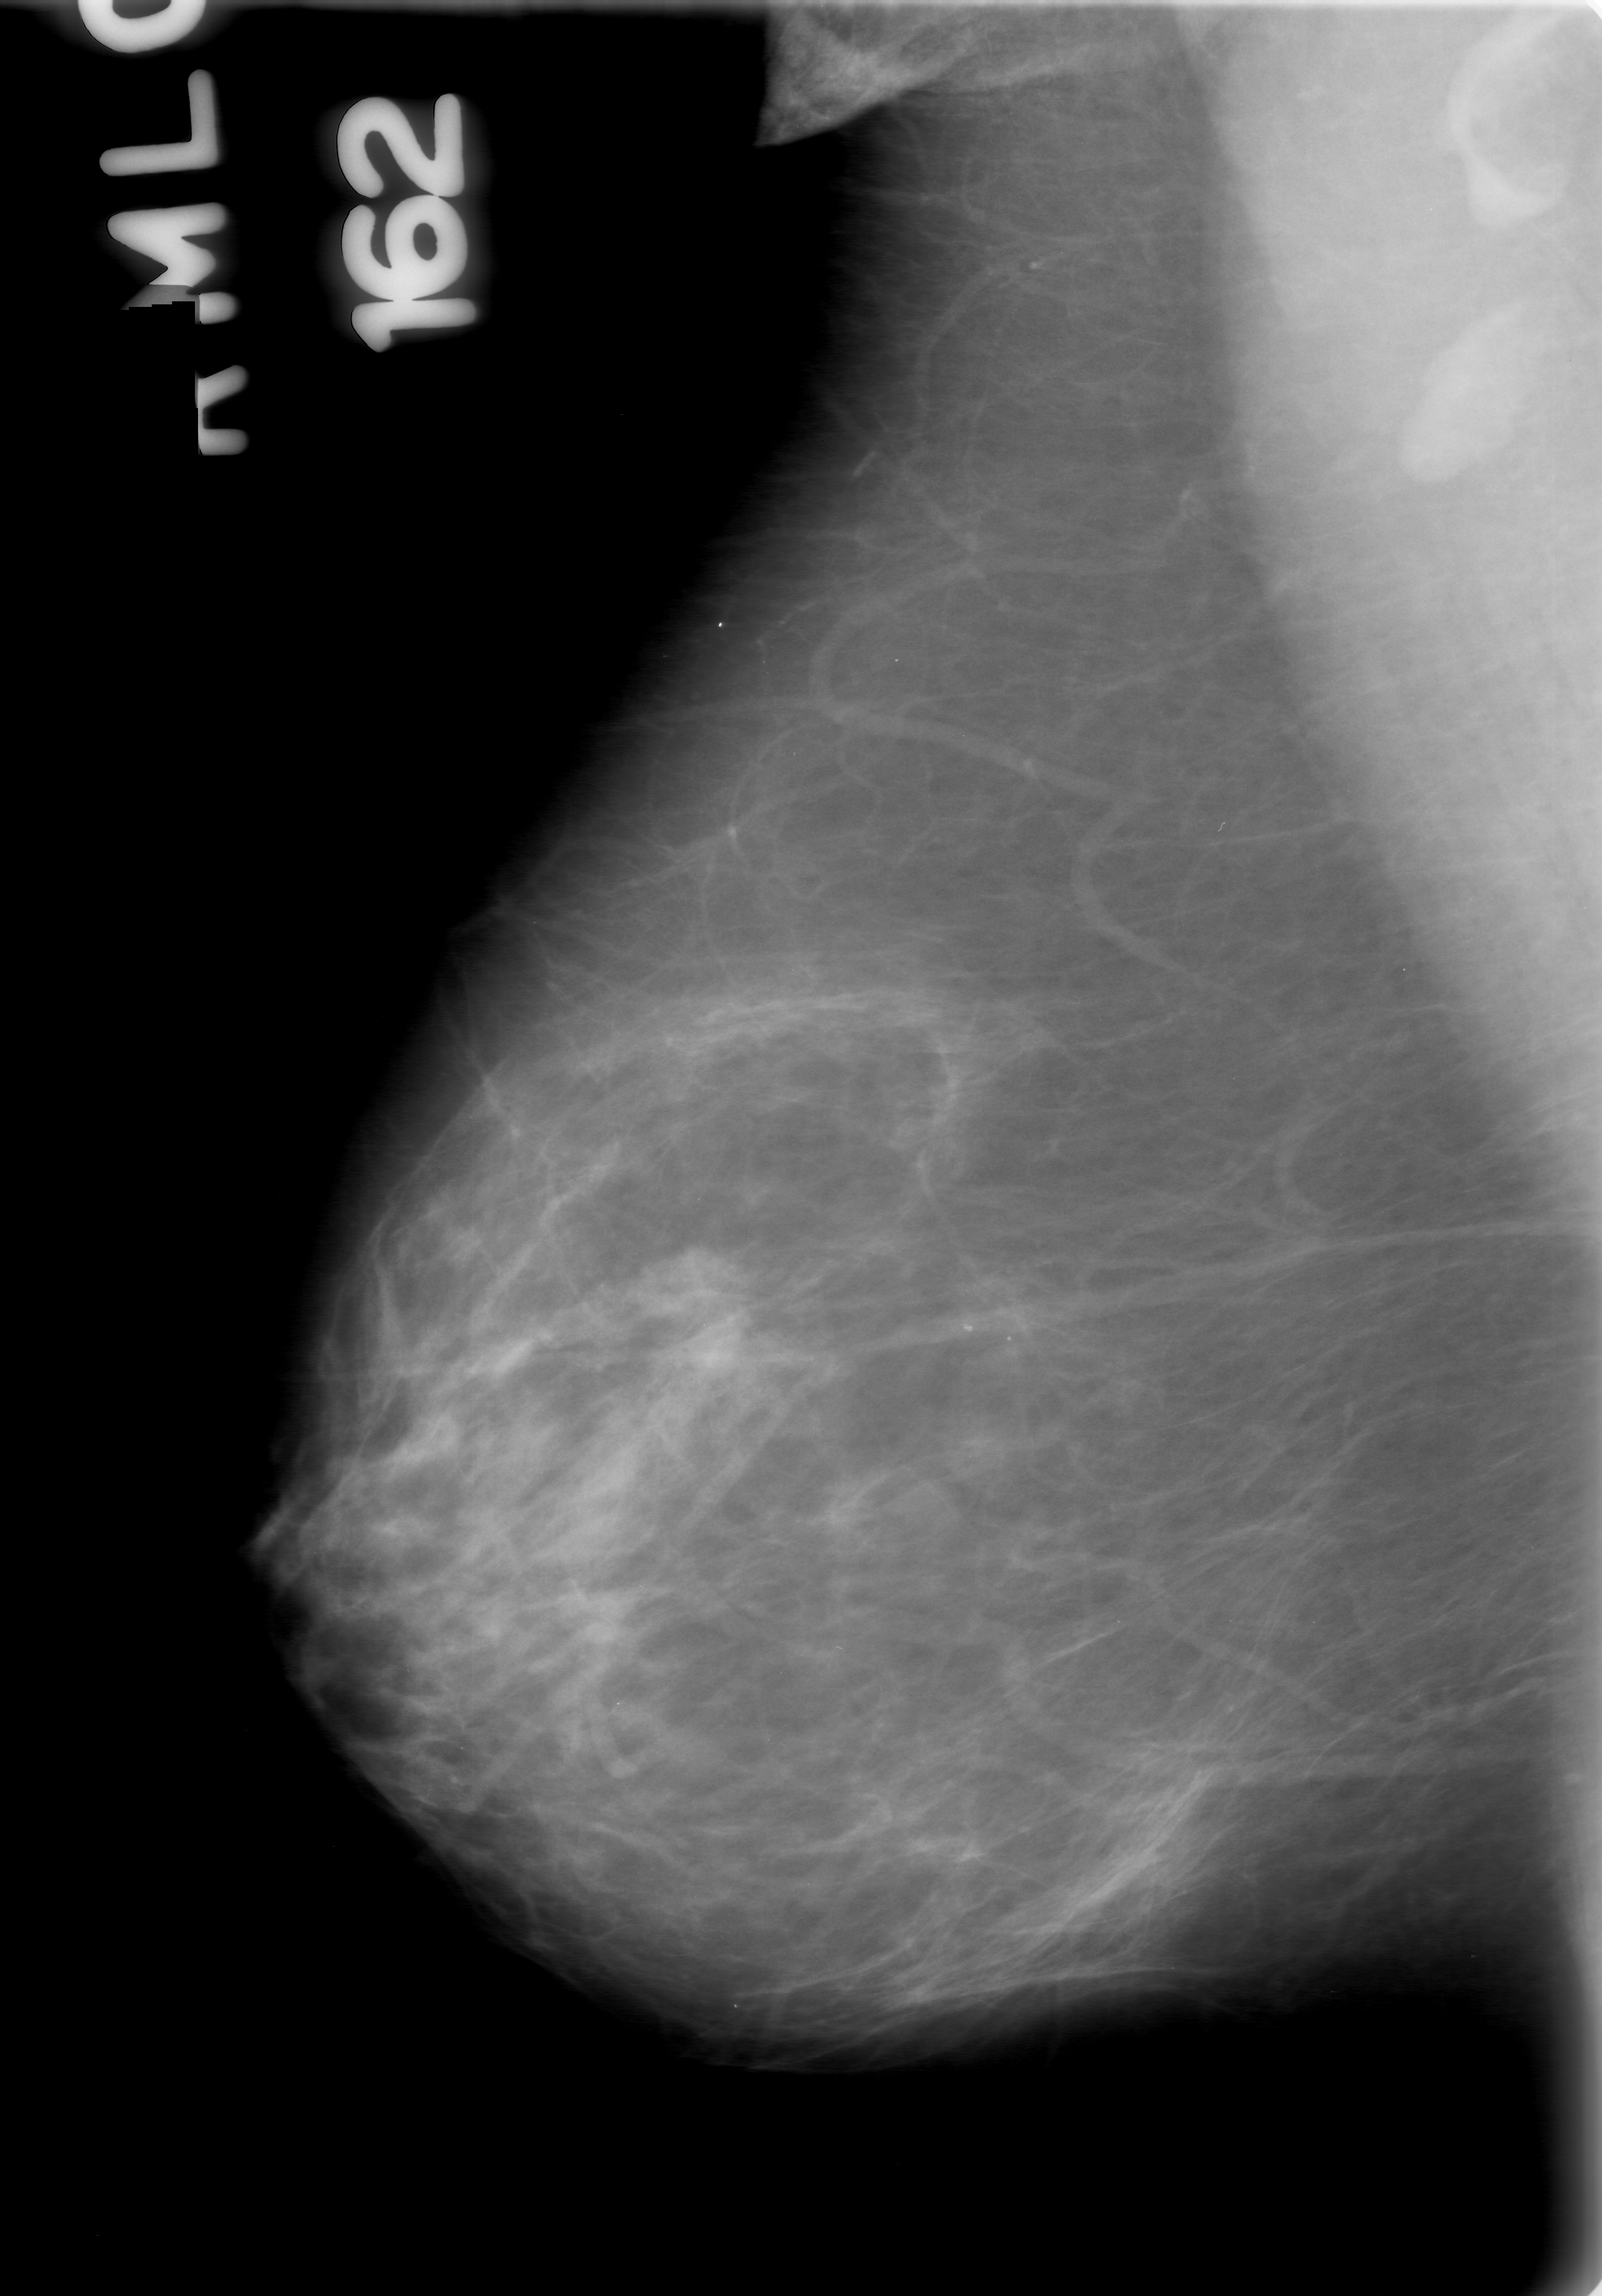
Scanned film-screen mammogram; right breast; MLO view; BI-RADS breast density category 2 (scale 1–4).
Radiologist-marked abnormalities on this image: mass, shape round, margins obscured; BI-RADS assessment category 0 (incomplete: needs additional imaging); pathology (as recorded): benign.